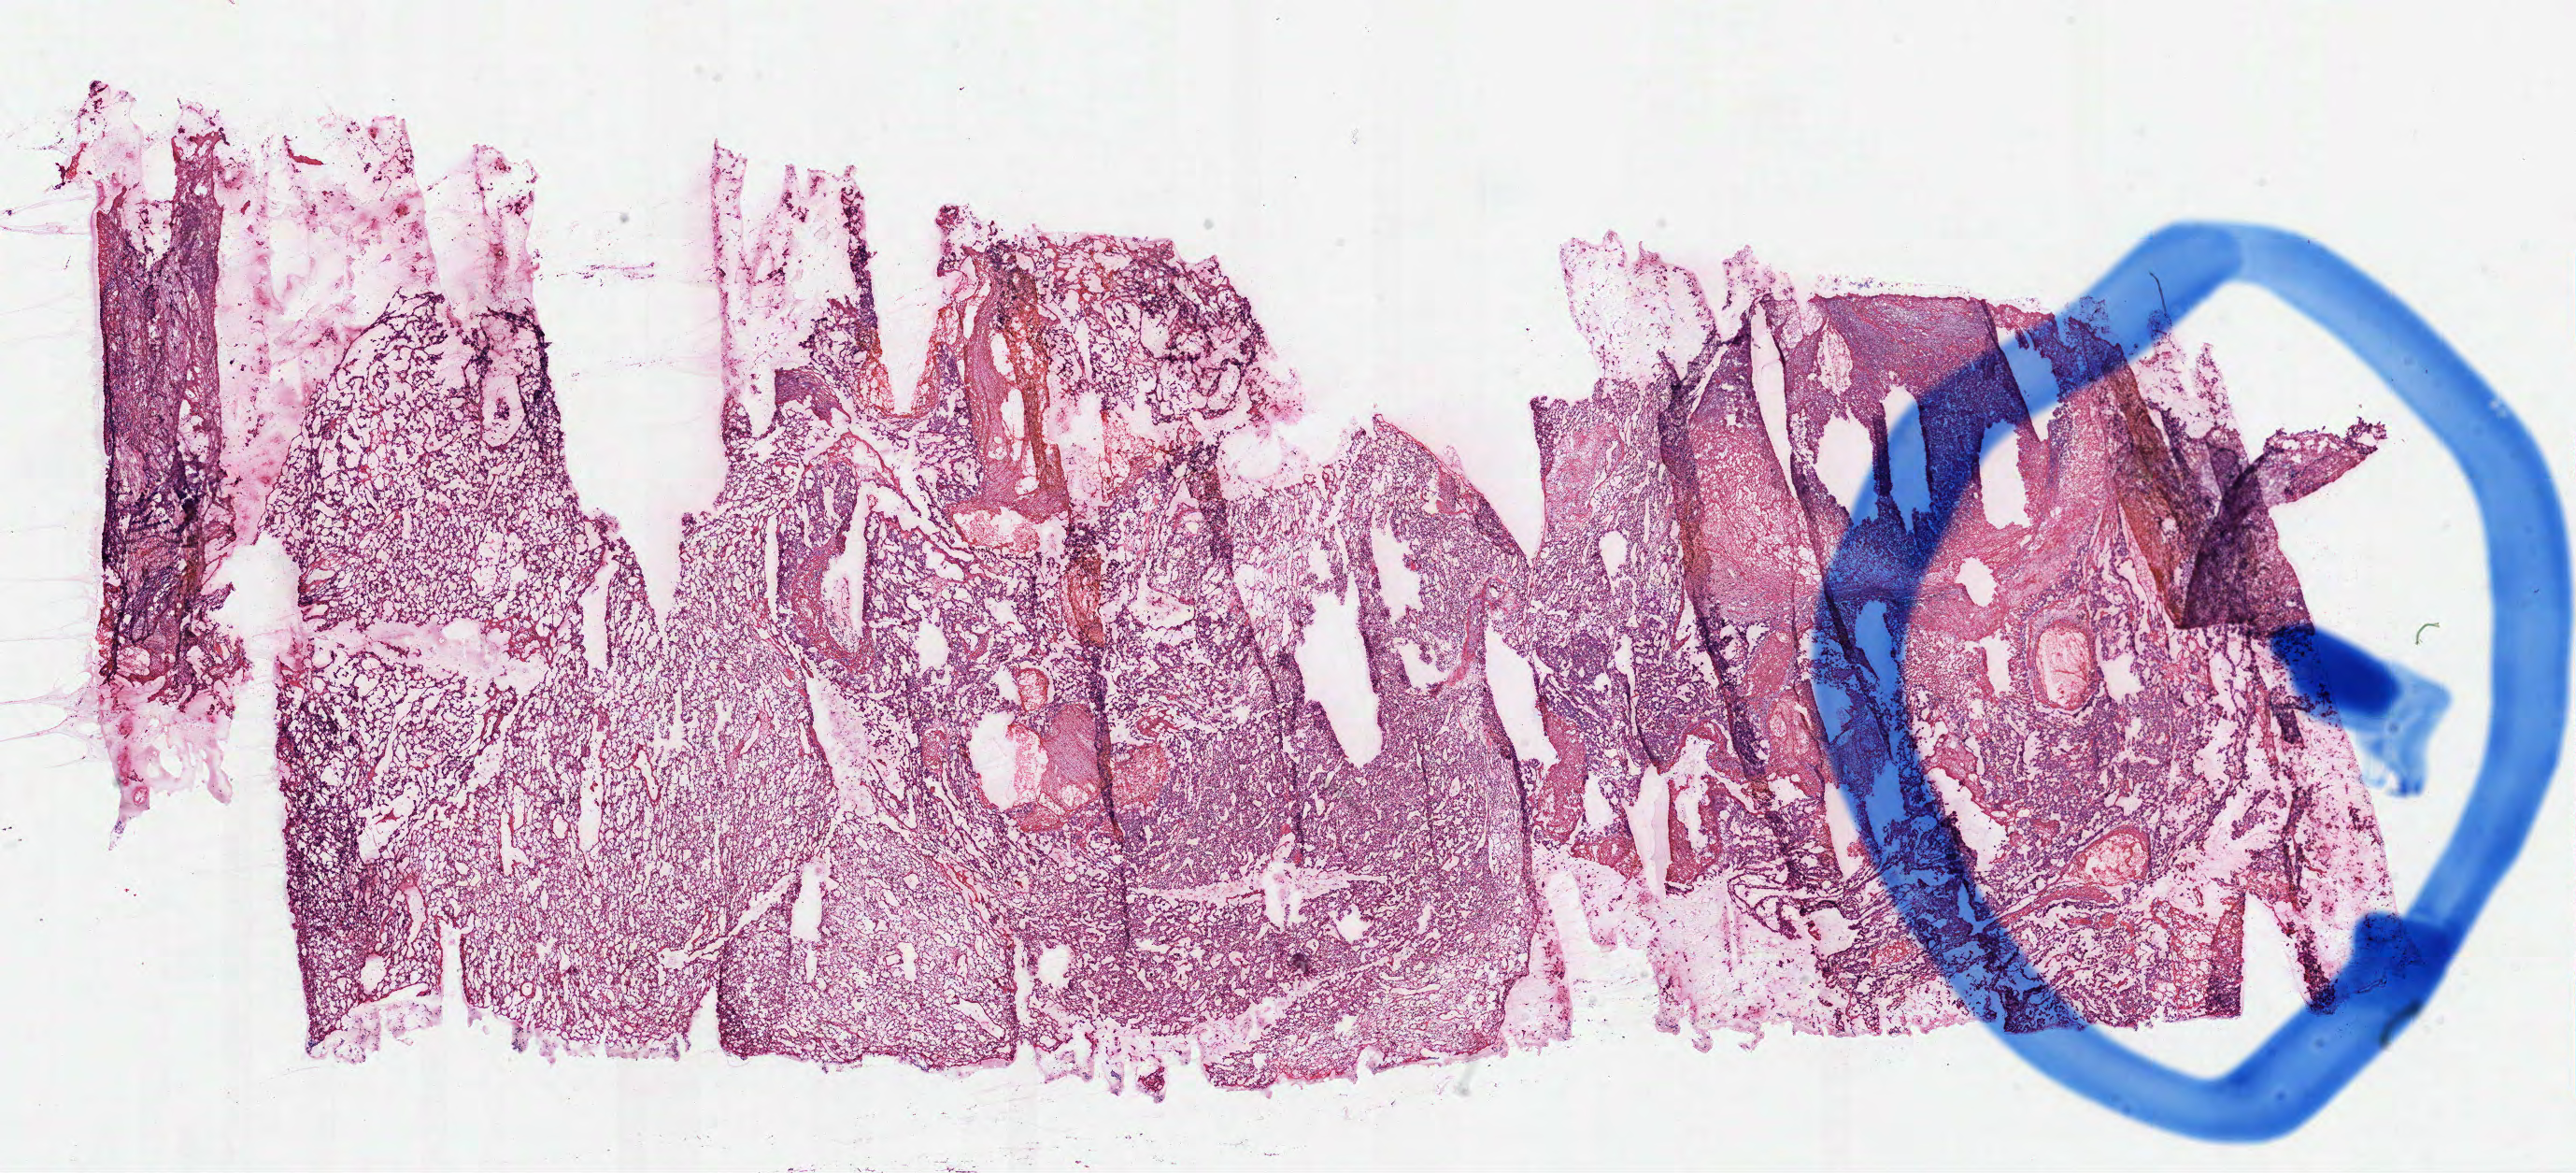
Digitized H&E tissue section (whole slide) — shown as a low-resolution overview of the whole scanned area (about 22.2 x 10.1 mm); frozen section from the top of the tissue portion; sample: primary tumour, kidney. Female patient; age at initial diagnosis 54 years. Histologic grade: G4 (undifferentiated). Slide review estimates, as recorded: tumour cells 85%, tumour nuclei 80%, normal cells 0%, stromal cells 15%, necrosis 0%.
AJCC pathologic stage: IV (6th edition). TNM: T3a N0 M1. Histologic diagnosis: Clear cell adenocarcinoma, NOS.